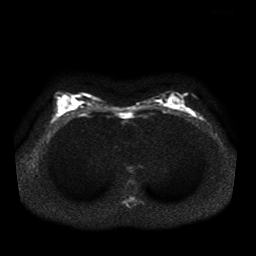
Breast MRI, one axial slice. Position 22 of 41 along the scan axis. Diffusion-weighted series; image 2 of 4 stored at this slice position (different b-values; order by instance number). 1.5 T. 5 mm slice thickness. 256 × 256 image matrix, field of view 330 × 330 mm. Female patient.
Structures marked on this image (manually delineated by an expert):
- tumour on diffusion-weighted imaging: bounding box [x1, y1, x2, y2] px = [186, 109, 191, 112]